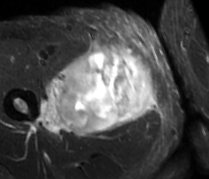
MRI of an extremity soft-tissue mass, one axial slice. Position 38 of 89 along the scan axis. STIR. MR volume resampled by the dataset authors to the PET/CT grid (not the native acquisition matrix). 3.27 mm slice thickness. 209 × 179 image matrix, field of view 204 × 175 mm. Male patient. Case-level facts recorded for this patient, not image findings: histological type: undifferentiated - pleiomorphic; grade: high; site of the primary tumour: right thigh.
Annotated regions visible in this slice (expert contour drawn on MRI and transferred to this co-registered scan by the dataset authors):
- gross tumour volume including surrounding oedema: bounding box [x1, y1, x2, y2] px = [37, 44, 156, 136]
- gross tumour volume (mass): [57, 44, 156, 136]